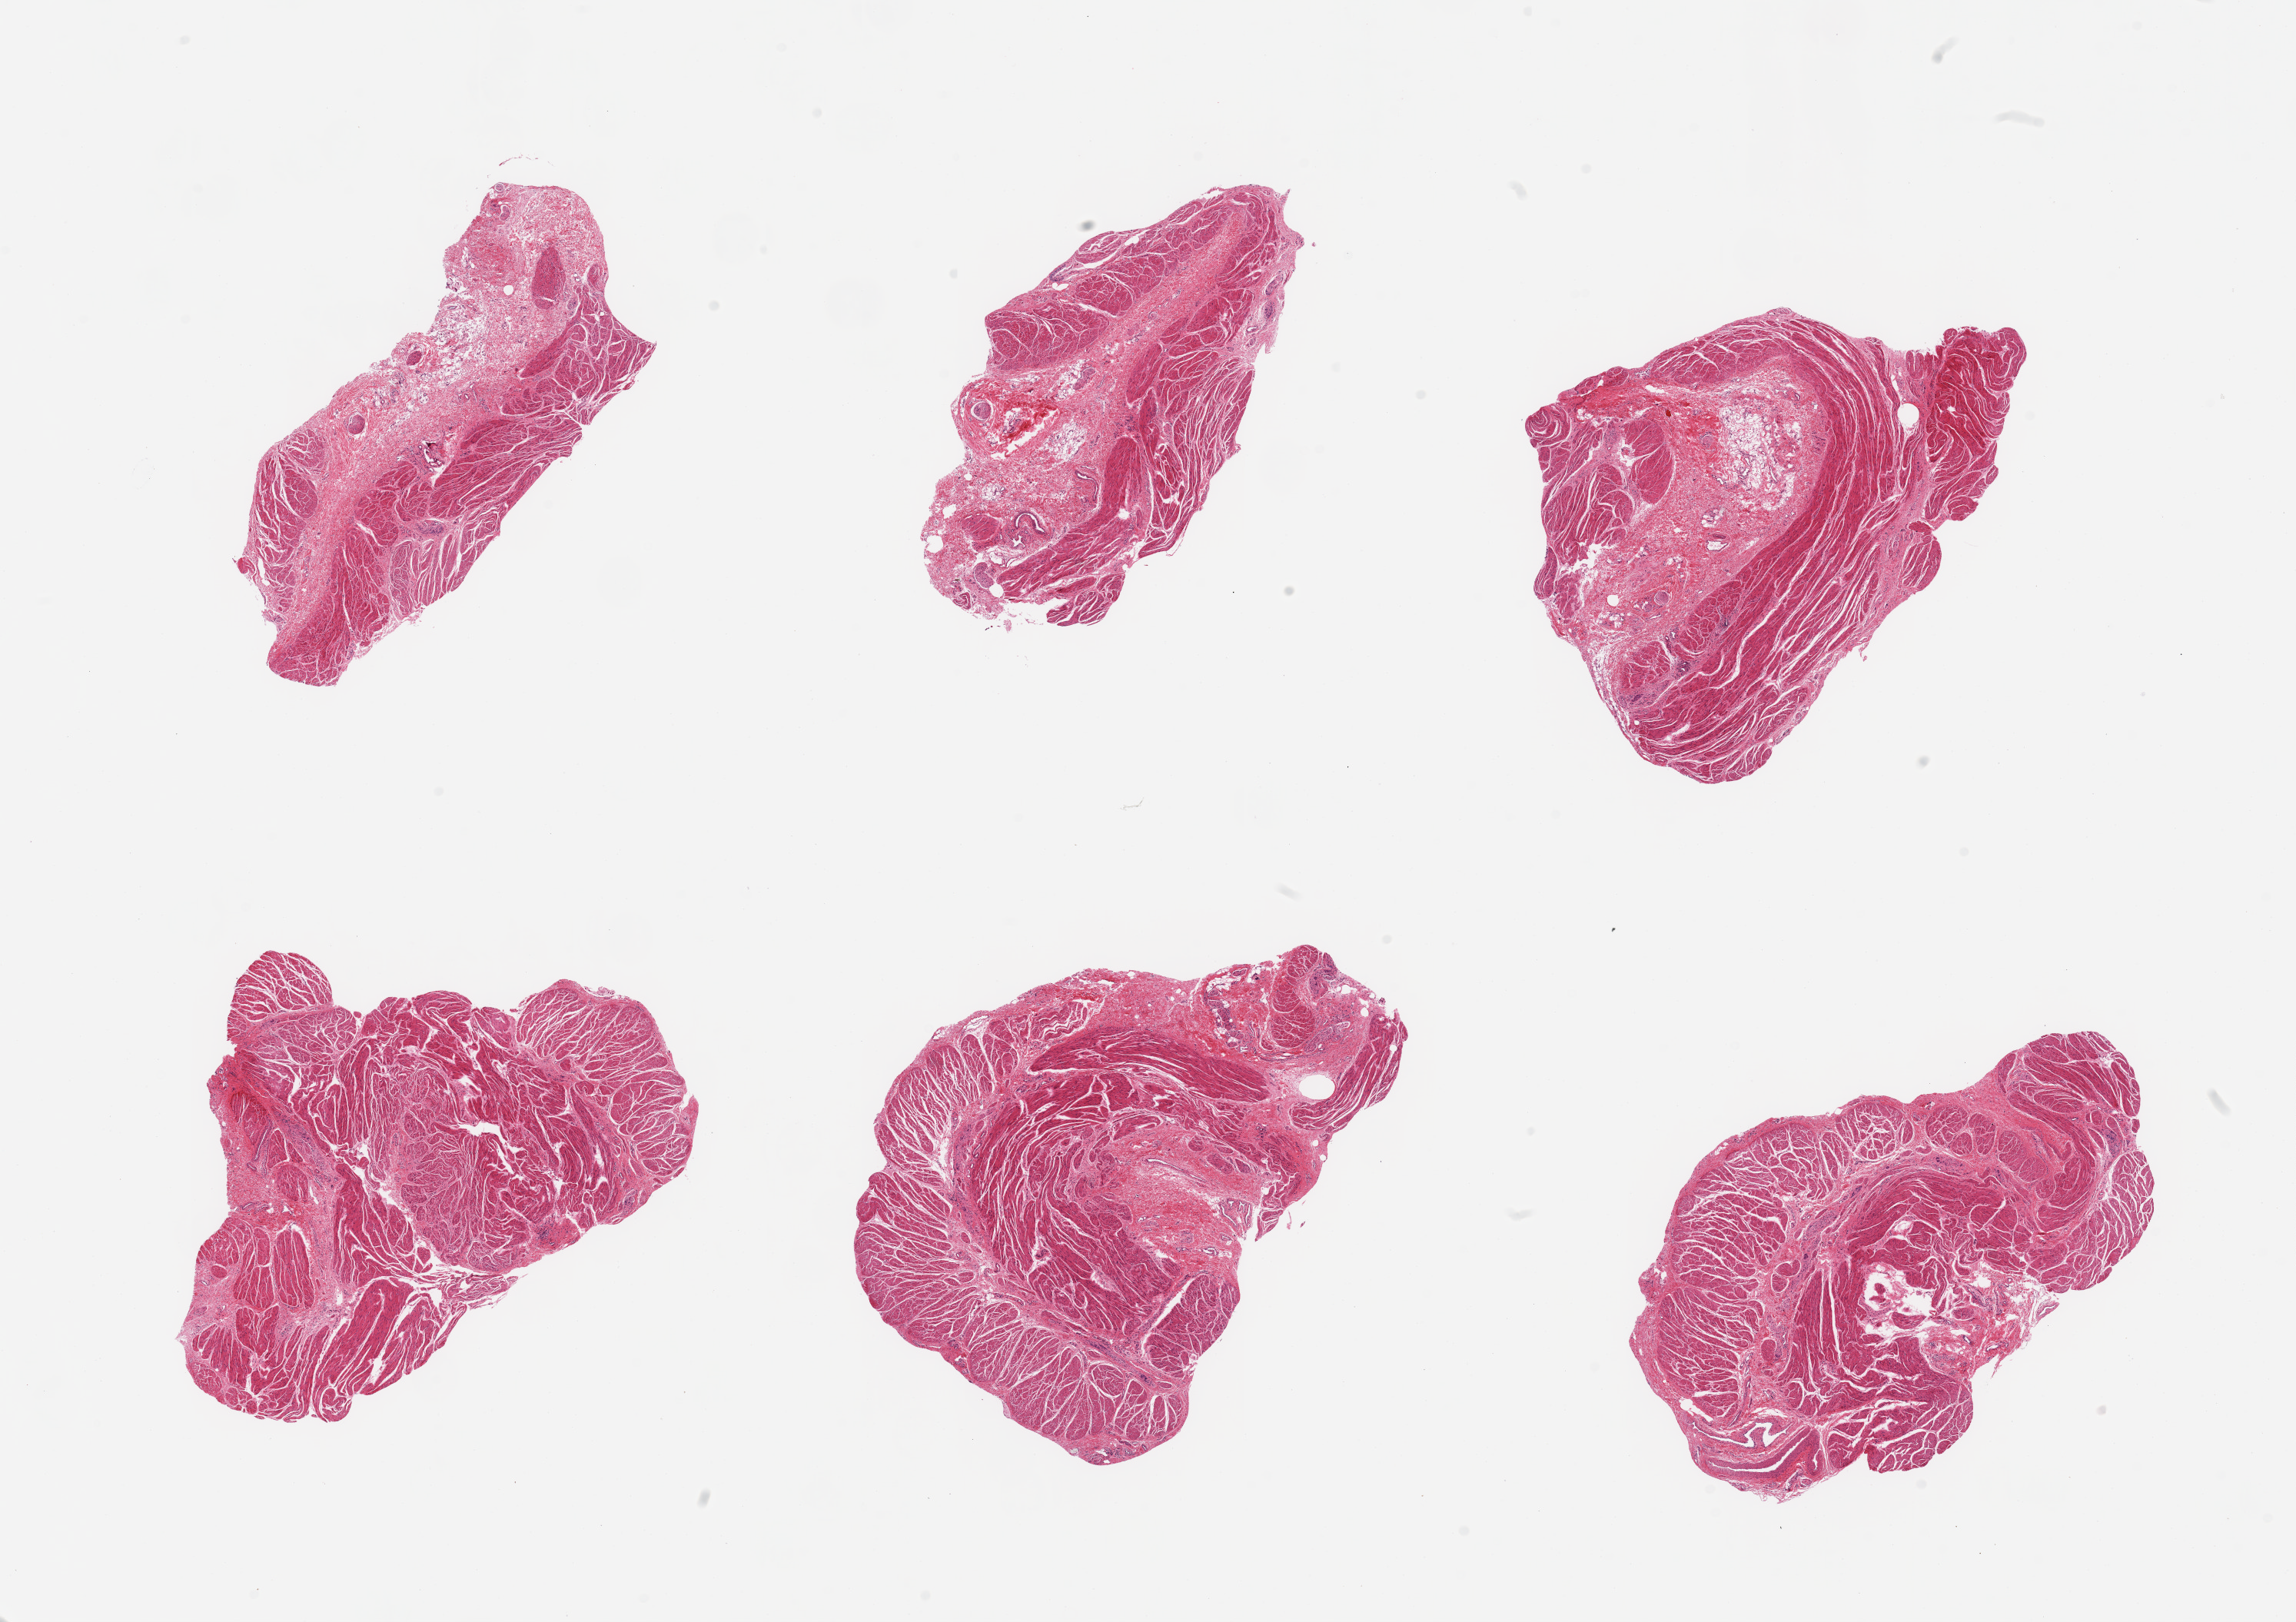
Hematoxylin and eosin (H&E) whole-slide image, a low-resolution overview of the entire scanned area, about 23.6 x 16.7 mm (slide scanned at 20x). PAXgene-fixed paraffin-embedded (PFPE) section. Section of gastroesophageal junction (target tissue). Donor tissue sample. Donor: male.
Reviewer comment on this tissue sample: 6 pieces; up to 40% adventitial stromal content.